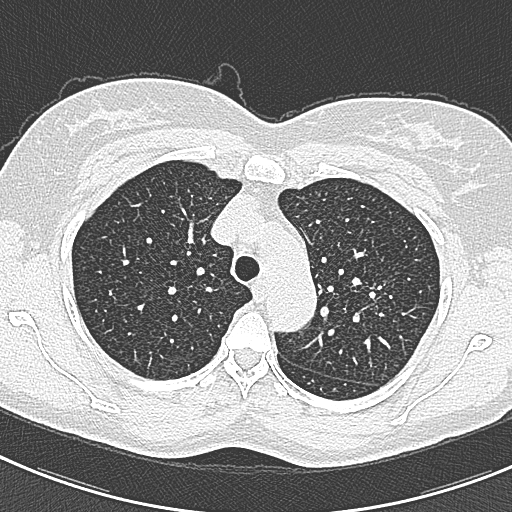
Axial slice from a low-dose chest CT screening exam. Baseline screening round. Lung window (W 1500 / L -600 HU). 1 mm slice thickness. Female, age 57 years at enrolment. Current smoker at enrolment.
Expert reader's lesion annotation, bounding box (x1, y1, x2, y2) in pixels: (361, 267, 413, 325). The screening reader recorded 2 non-calcified nodules or masses ≥4 mm on this exam (right lower lobe, left upper lobe); which of them this box marks is not recorded. Lung cancer was diagnosed 198 days after this screen: adenocarcinoma, NOS, left upper lobe, well differentiated (G1), stage IA (AJCC 6th edition), 10 mm at pathology.